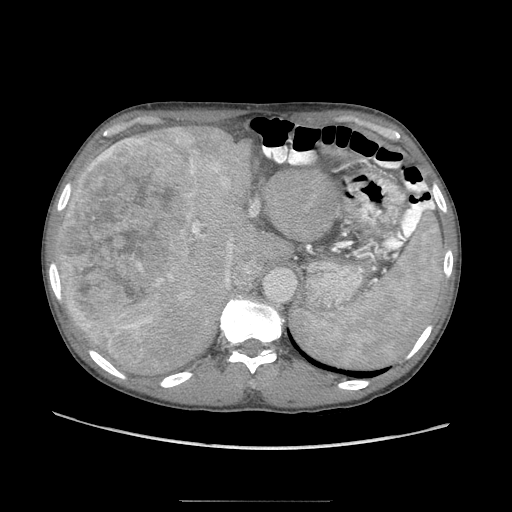
Contrast-enhanced abdominal CT (liver protocol), one axial slice; slice 67 of 103 in the series (ordered by position); reconstruction kernel STANDARD; soft-tissue window (W 400 / L 40 HU); 2.5 mm slice thickness; 512 × 512 image matrix. From the clinical record (not read from this slice): diagnosis: hepatocellular carcinoma (patient treated with transarterial chemoembolisation; whether this scan precedes or follows treatment is not stated here); TNM stage (as recorded): Stage-IIIA; Child-Pugh class: A; tumour differentiation: moderately differentiated; tumour nodularity: multinodular.
Outlined on this slice (semi-automatically segmented with operator editing):
- liver parenchyma outside the tumour (the mass and vessels are separate outlines, so this box may not span the whole liver): bounding box <56,126,330,378> (left, top, right, bottom; pixels)
- mass: <61,138,235,369>
- liver vessels: <116,220,204,377>